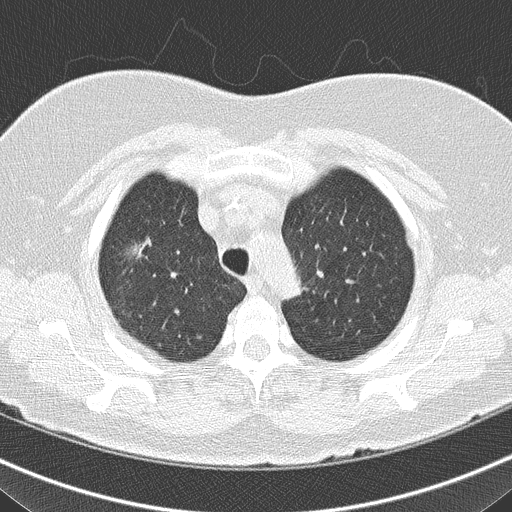
Chest CT (low-dose screening protocol), one axial image. Third screening round (two years after baseline). Lung window (W 1500 / L -600 HU). 2 mm slice thickness. Lung (sharp) reconstruction kernel (B50f). Slice 139 of 161 in the series. Female, age 74 years at enrolment. Former smoker at enrolment.
Expert reader's lesion annotation, box from (x=110, y=230) to (x=177, y=295) px. The screening reader recorded 5 non-calcified nodules or masses ≥4 mm on this exam (right upper lobe, right middle lobe, right middle lobe, left lower lobe, right lower lobe); which of them this box marks is not recorded. Participant outcome: lung cancer diagnosed 117 days after this screen — bronchiolo-alveolar carcinoma, non-mucinous, right upper lobe, well differentiated (G1), stage IA (AJCC 6th edition), 14 mm at pathology.